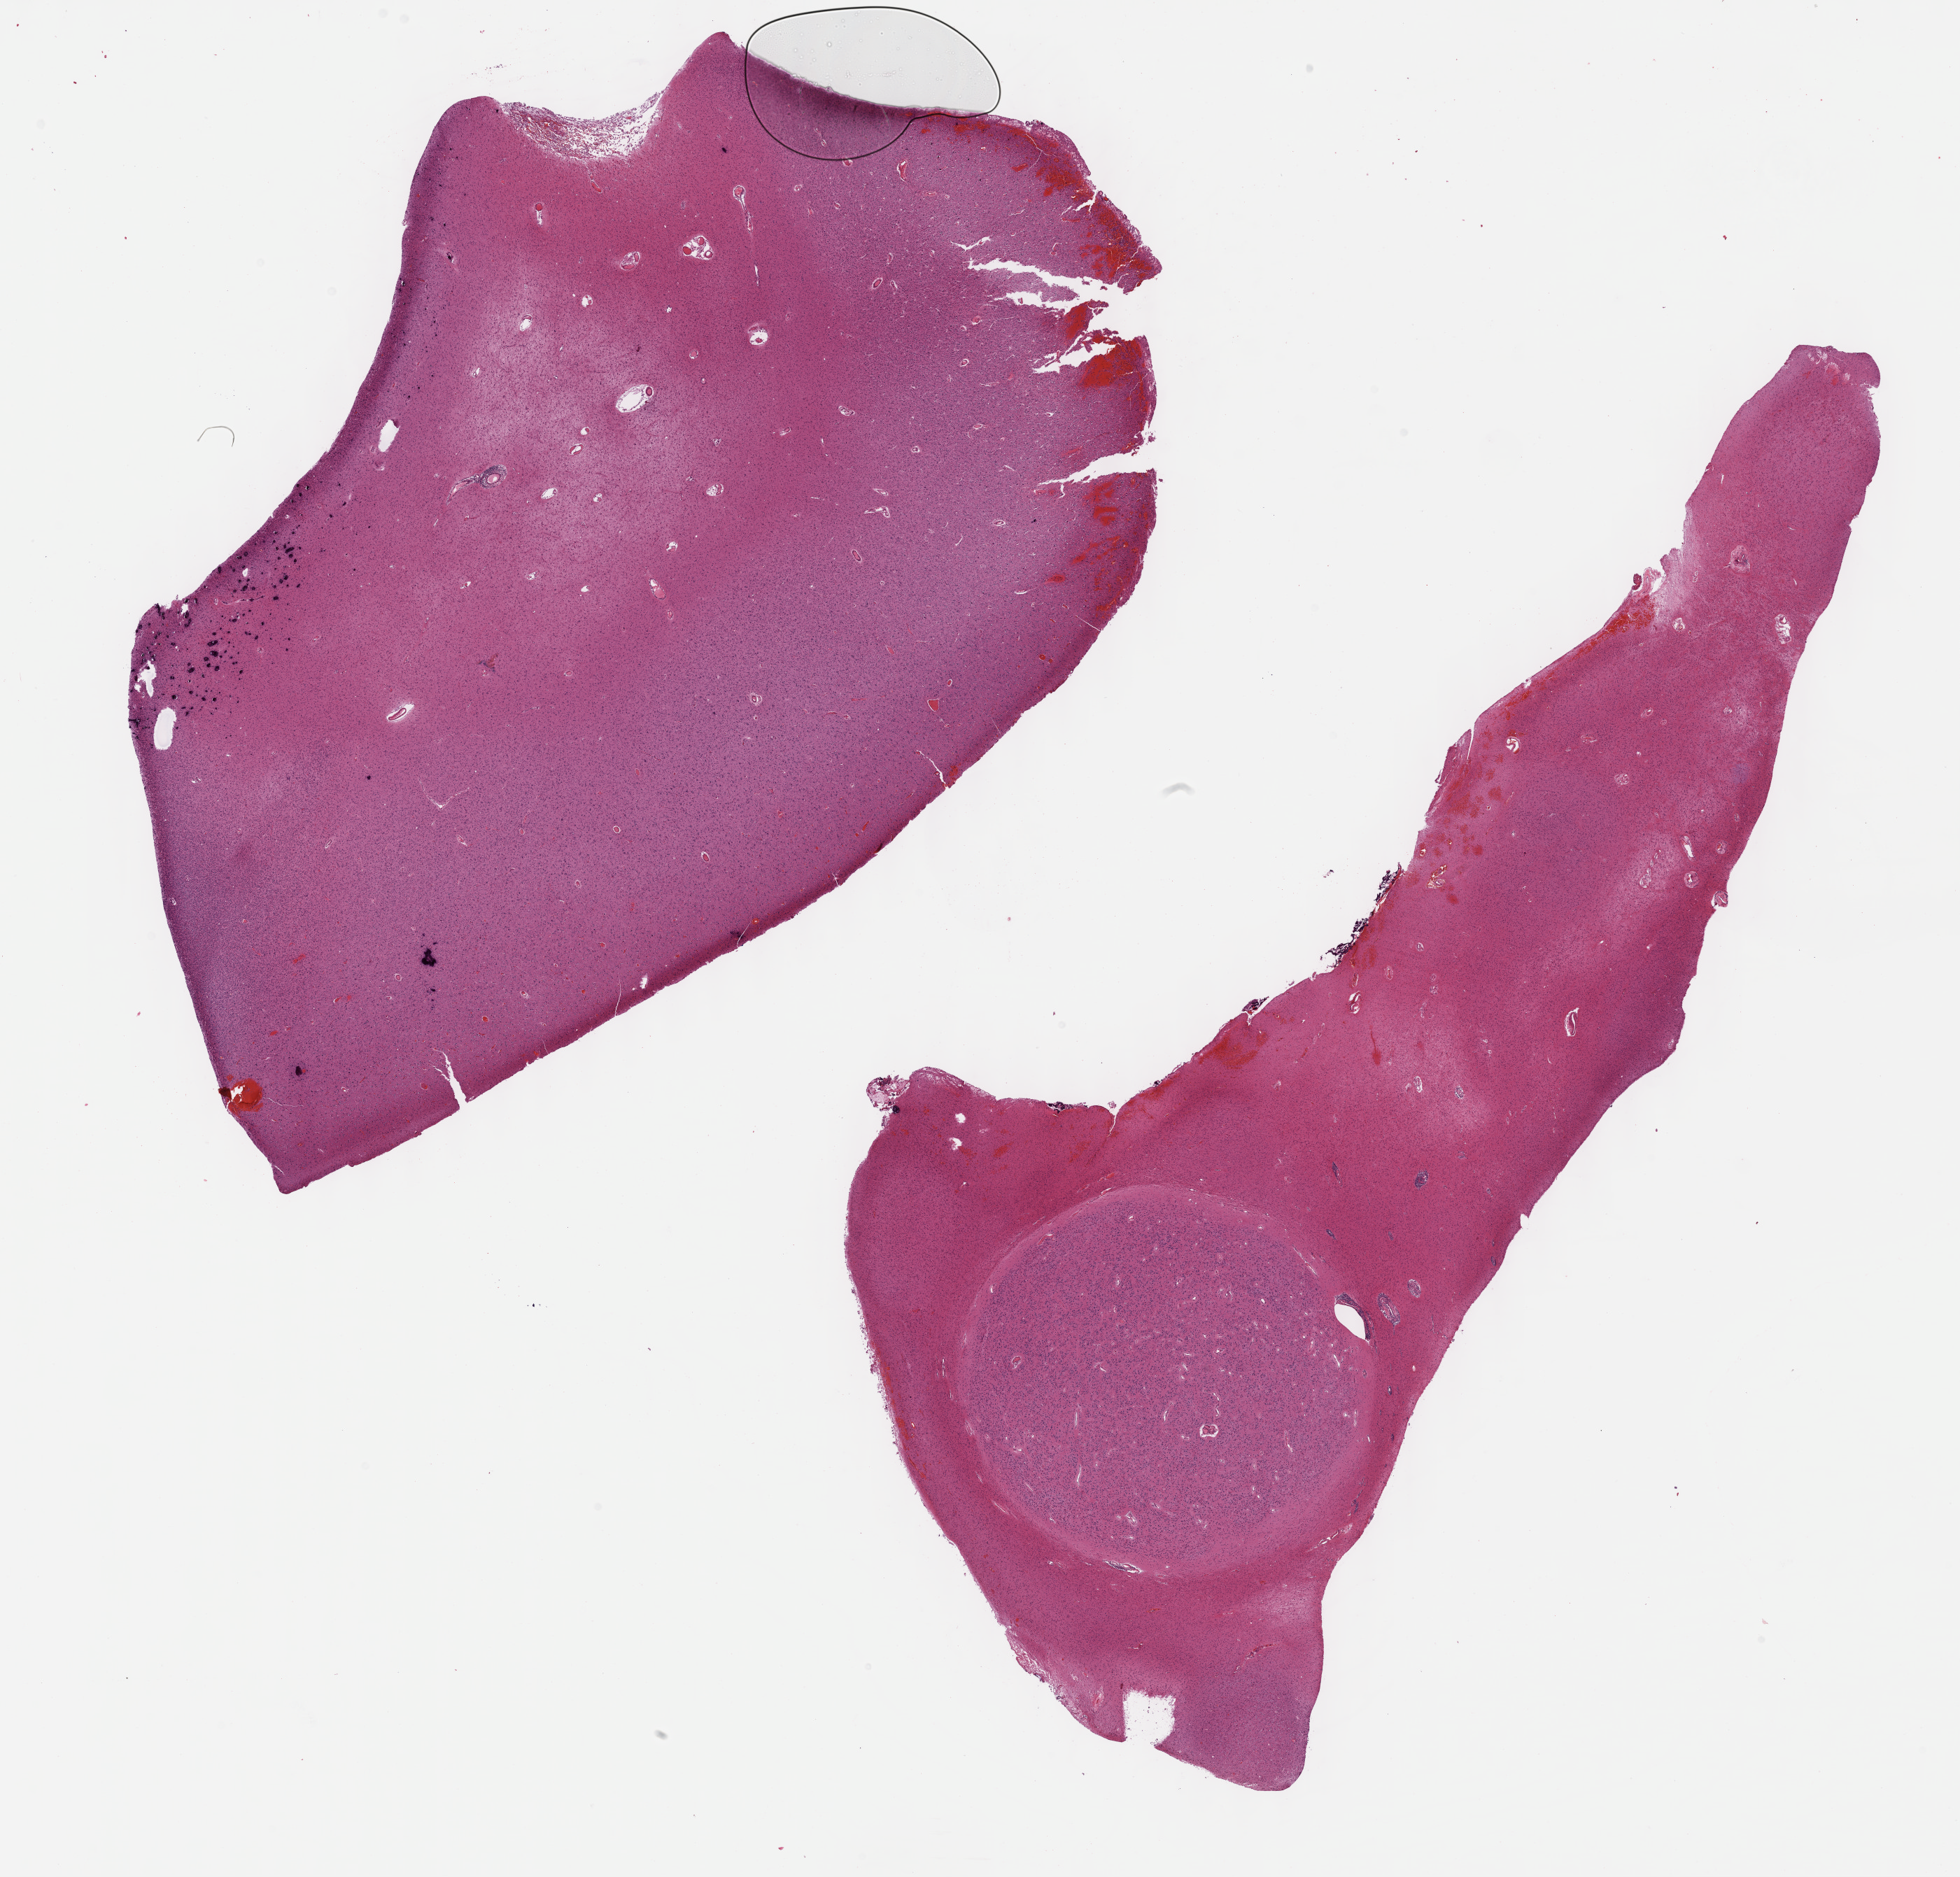
H&E whole-slide image — low-resolution overview of the scanned area, about 22.7 x 21.7 mm (from a 40x scan). FFPE section. Sample: primary tumour, brain. Male, age 53 years at initial diagnosis. Histologic grade: G3 (poorly differentiated).
Diagnosis: Oligodendroglioma, anaplastic (cerebrum).